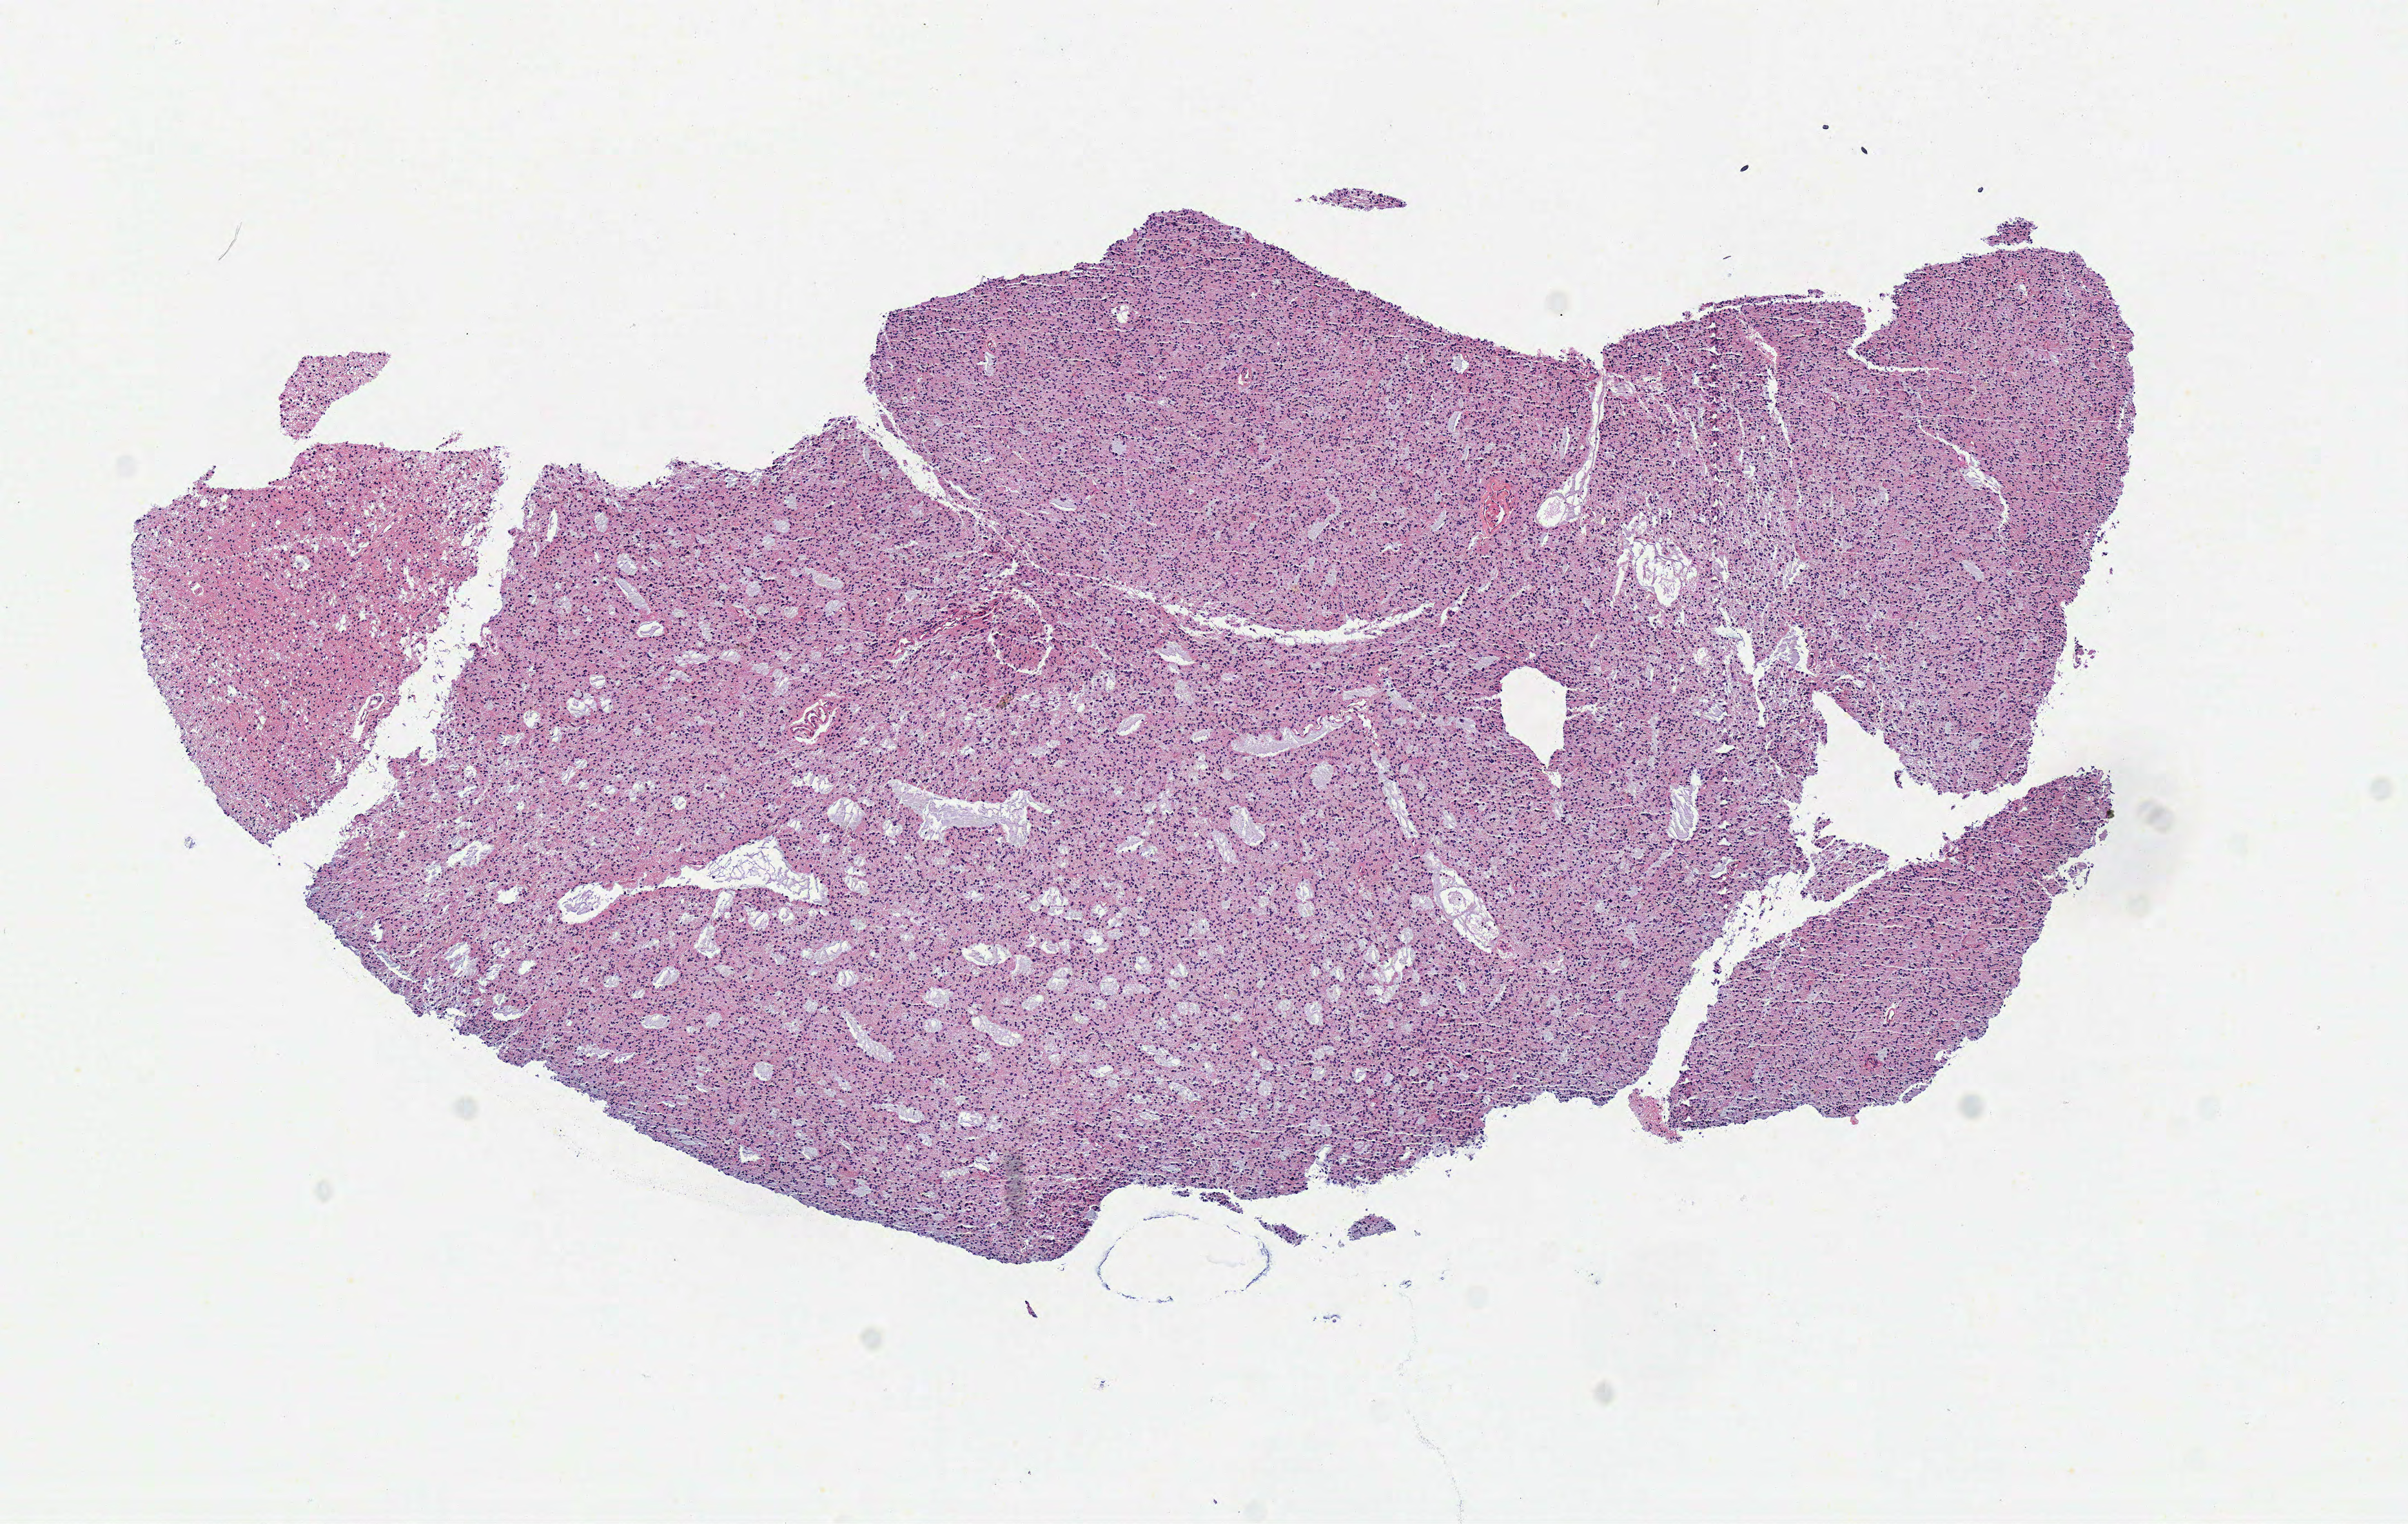
H&E whole-slide image, a low-resolution overview of the entire scanned area, about 7.3 x 4.6 mm (slide scanned at 40x). Frozen section from the top of the tissue portion. Sample: primary tumour, brain. Patient: male, age at initial diagnosis 31 years. Histologic grade: G2 (moderately differentiated). Pathologist review of this section (percent, as recorded): tumour cells 100%, tumour nuclei 80%, normal cells 0%, stromal cells 0%, necrosis 0%.
* diagnosis: Mixed glioma (cerebrum)